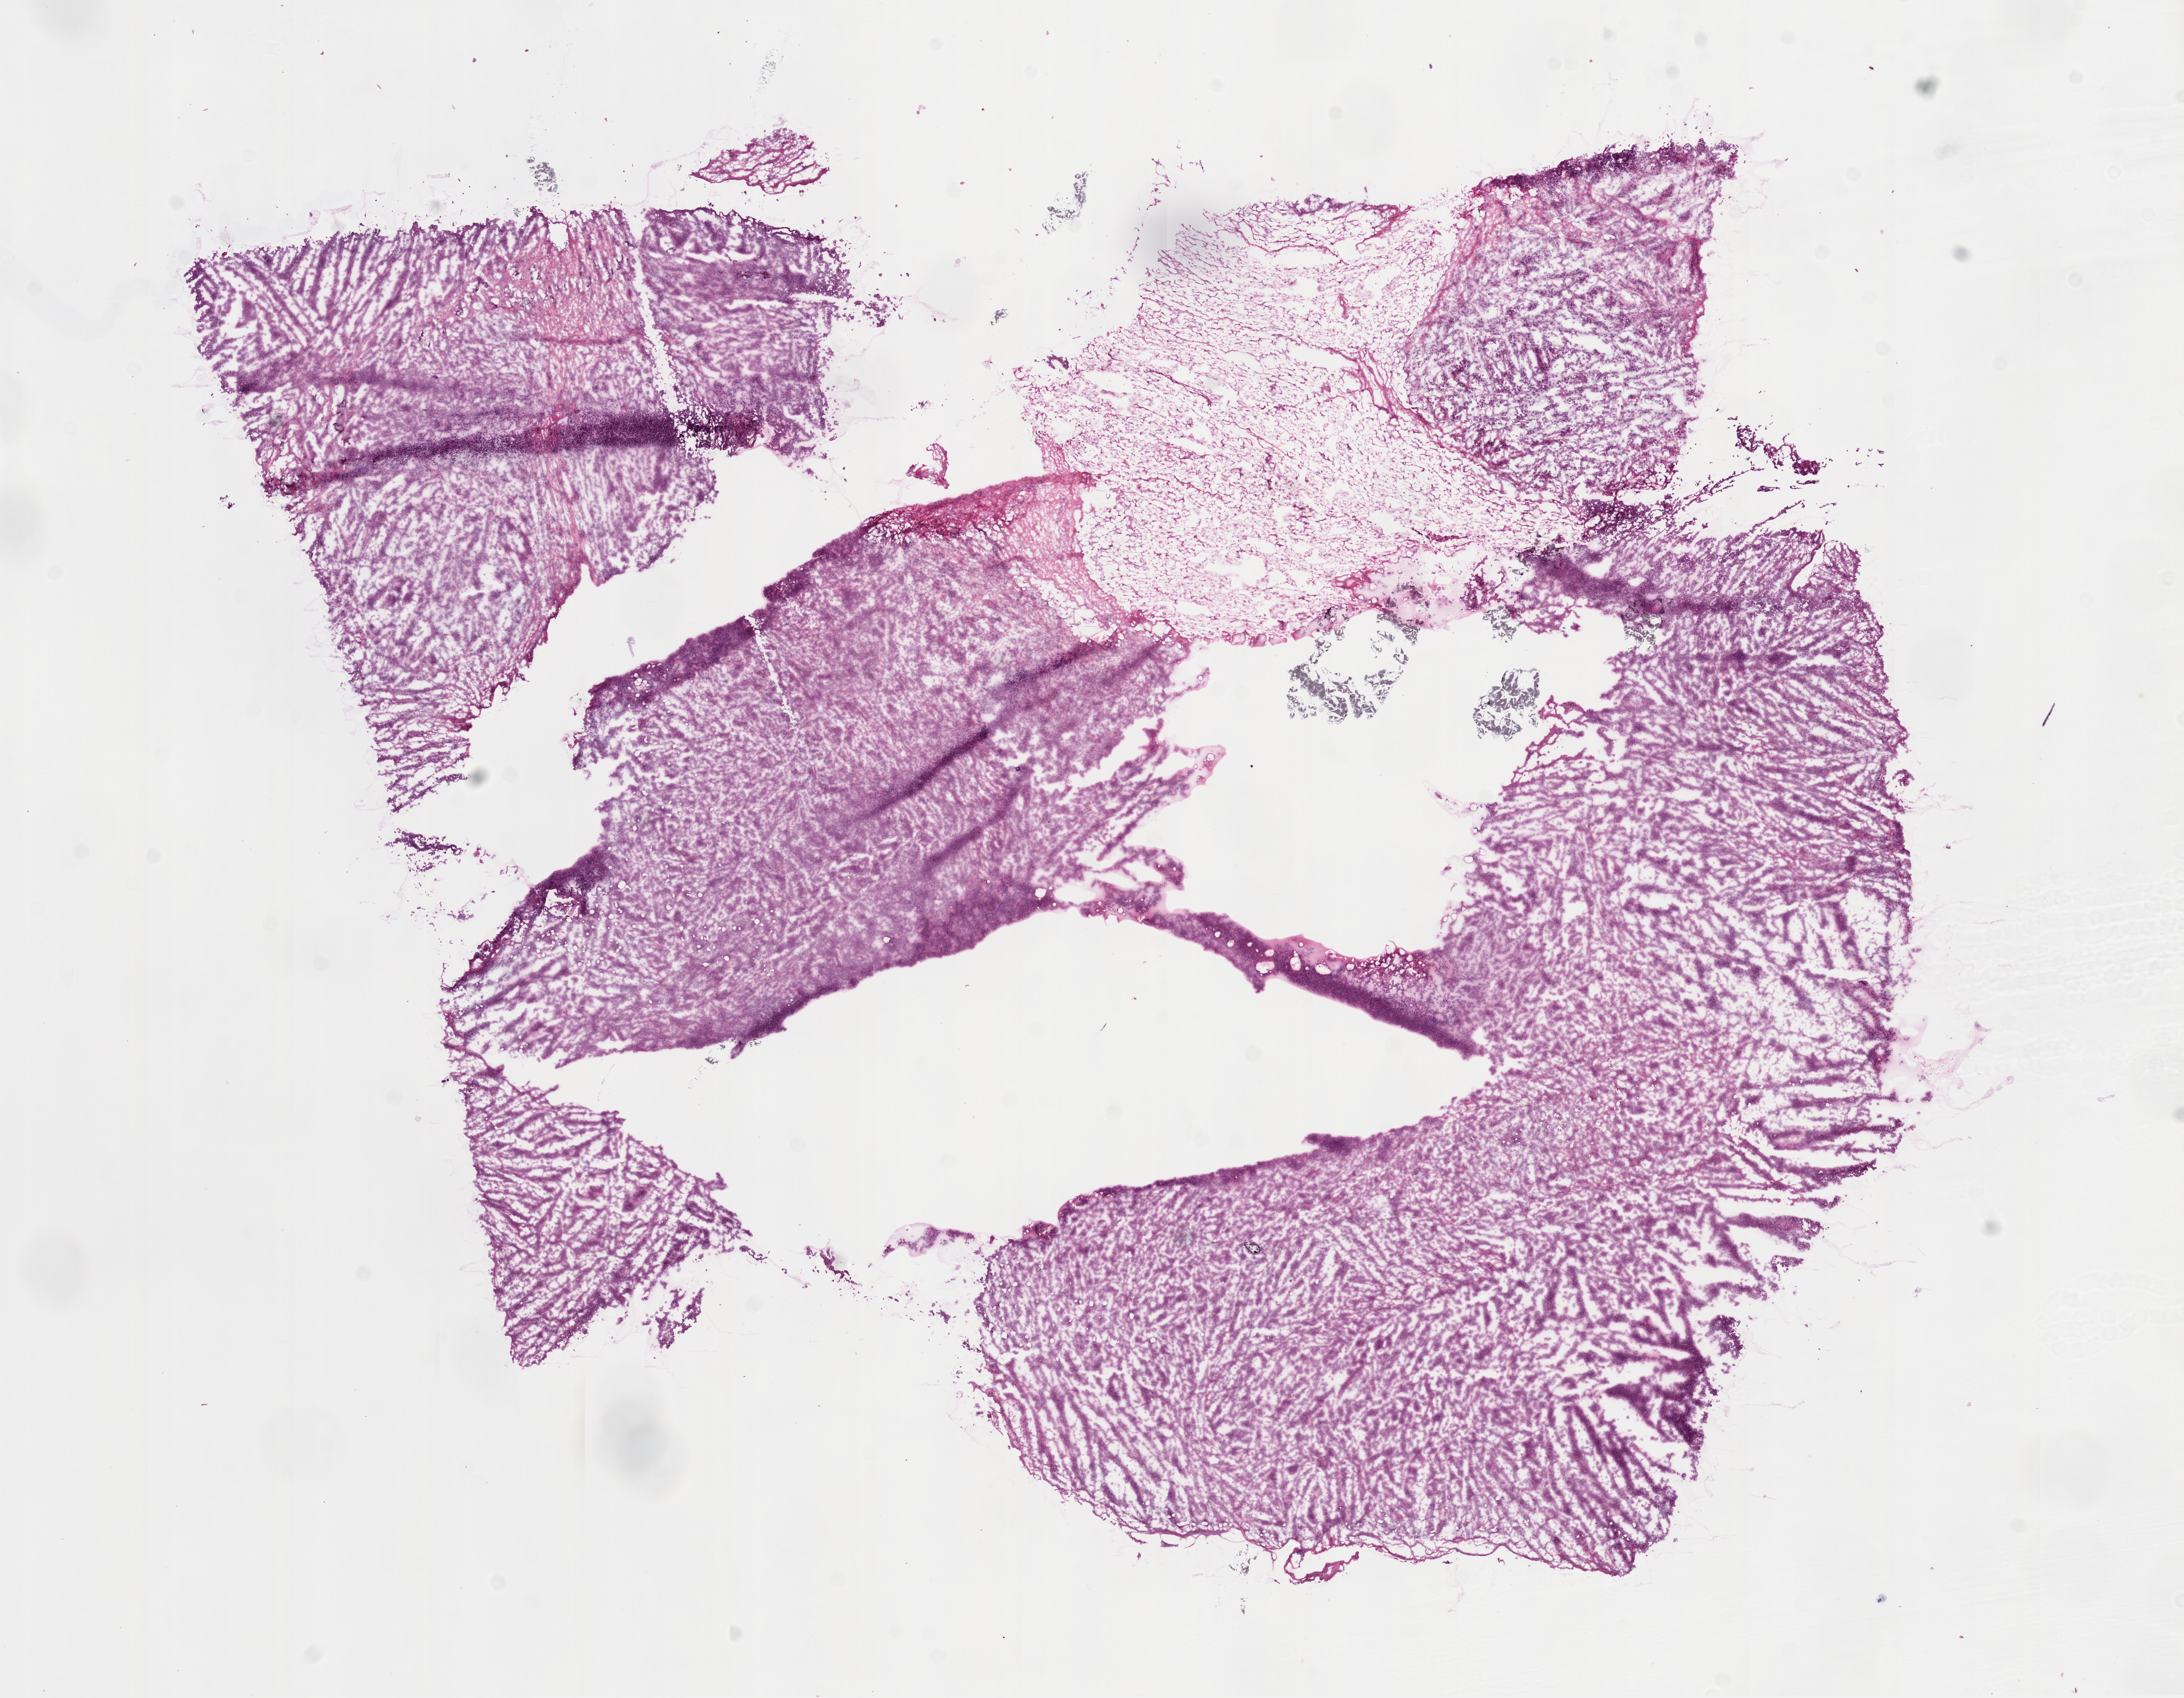
Whole-slide histology image, H&E-stained, whole scanned area (about 15.0 x 11.7 mm) shown as a low-resolution overview; frozen section from the top of the tissue portion; sample: primary tumour, lung. Male patient; age at initial diagnosis 71 years. Slide review estimates, as recorded: tumour cells 80%, tumour nuclei 80%.
Diagnosis: Adenocarcinoma, NOS.